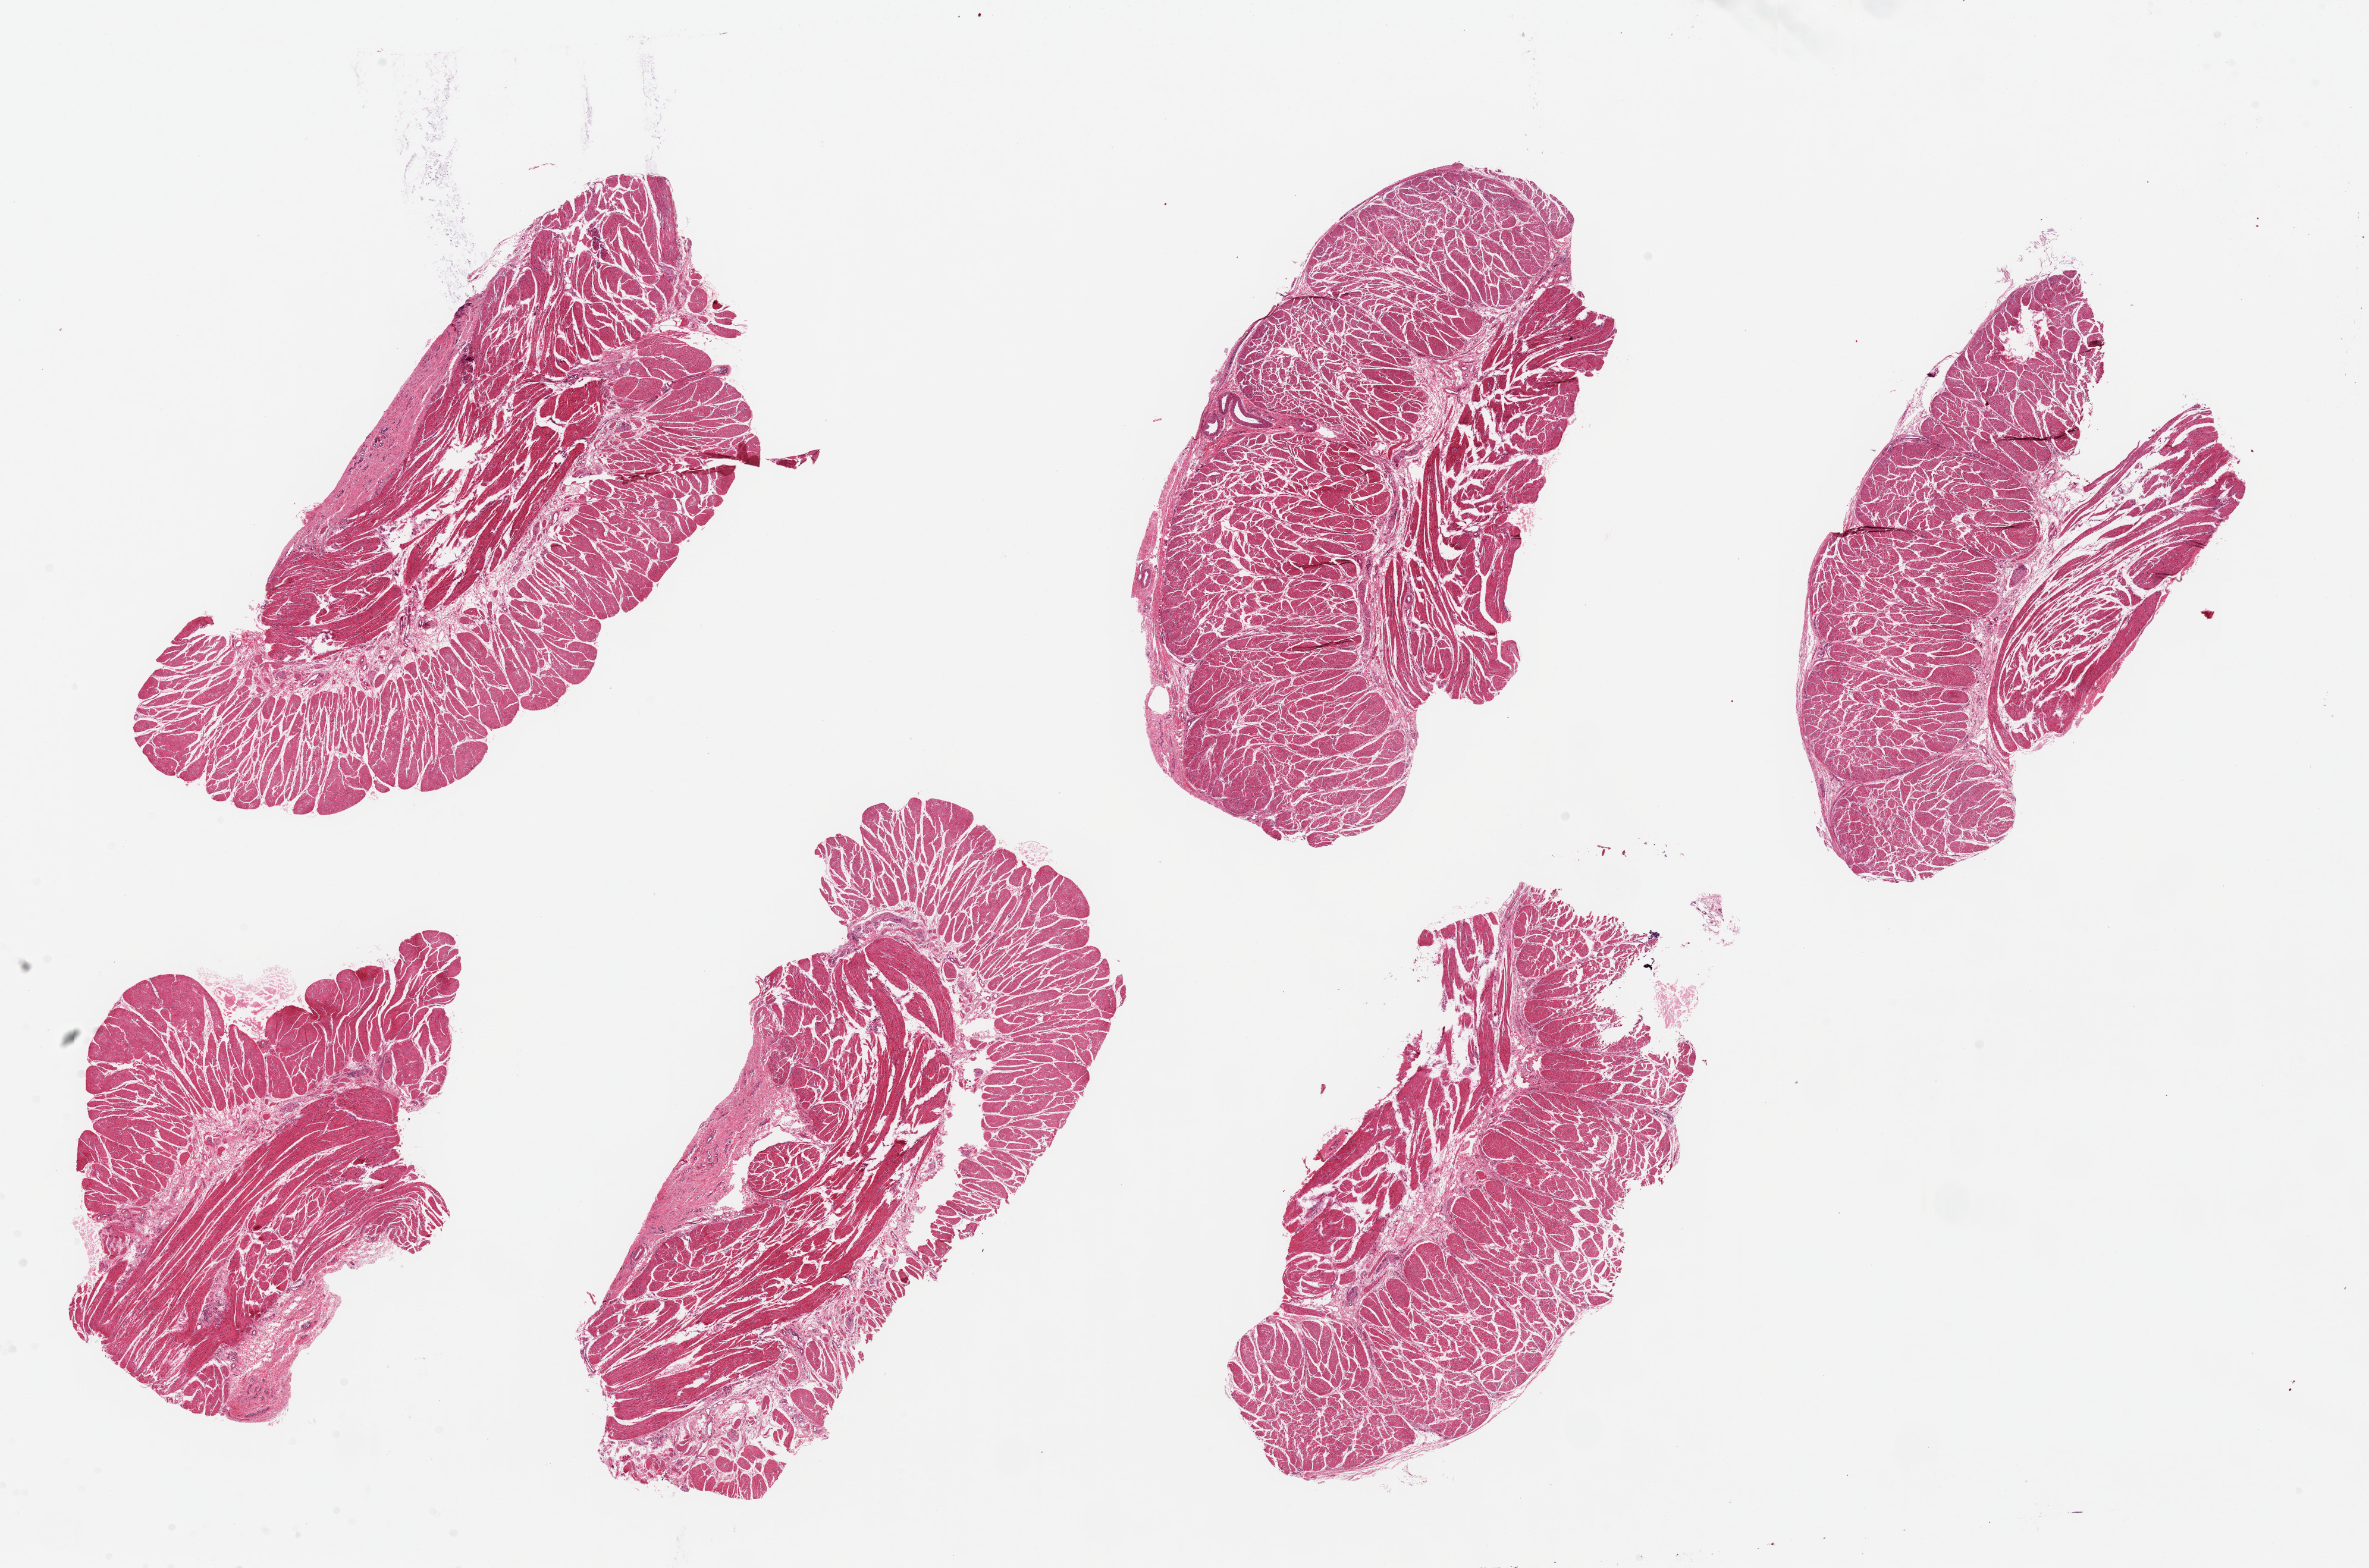
Whole-slide image, haematoxylin and eosin stain, shown as a low-resolution overview of the whole scanned area (about 31.5 x 20.9 mm); PAXgene-fixed paraffin-embedded (PFPE) section; sampled site (target tissue): esophageal muscle; donor tissue sample. Donor sex: male.
* reviewer comment on this tissue sample: 6 pieces, up to 10x5mm; all muscularis, good specimens